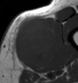
MRI of an extremity soft-tissue mass, one axial slice. Slice 19 of 43 in the series (ordered by position). MR volume resampled by the dataset authors to the PET/CT grid (not the native acquisition matrix). 78 × 83 image matrix, field of view 76 × 81 mm. Male patient. Case-level facts recorded for this patient, not image findings: histological type: pleiomorphic leiomyosarcoma; grade: high; site of the primary tumour: left thigh.
Annotated regions visible in this slice (expert contour drawn on MRI and transferred to this co-registered scan by the dataset authors):
- gross tumour volume including surrounding oedema: box from (x=13, y=17) to (x=60, y=68) px
- gross tumour volume (mass): (x=13, y=17)–(x=55, y=68)